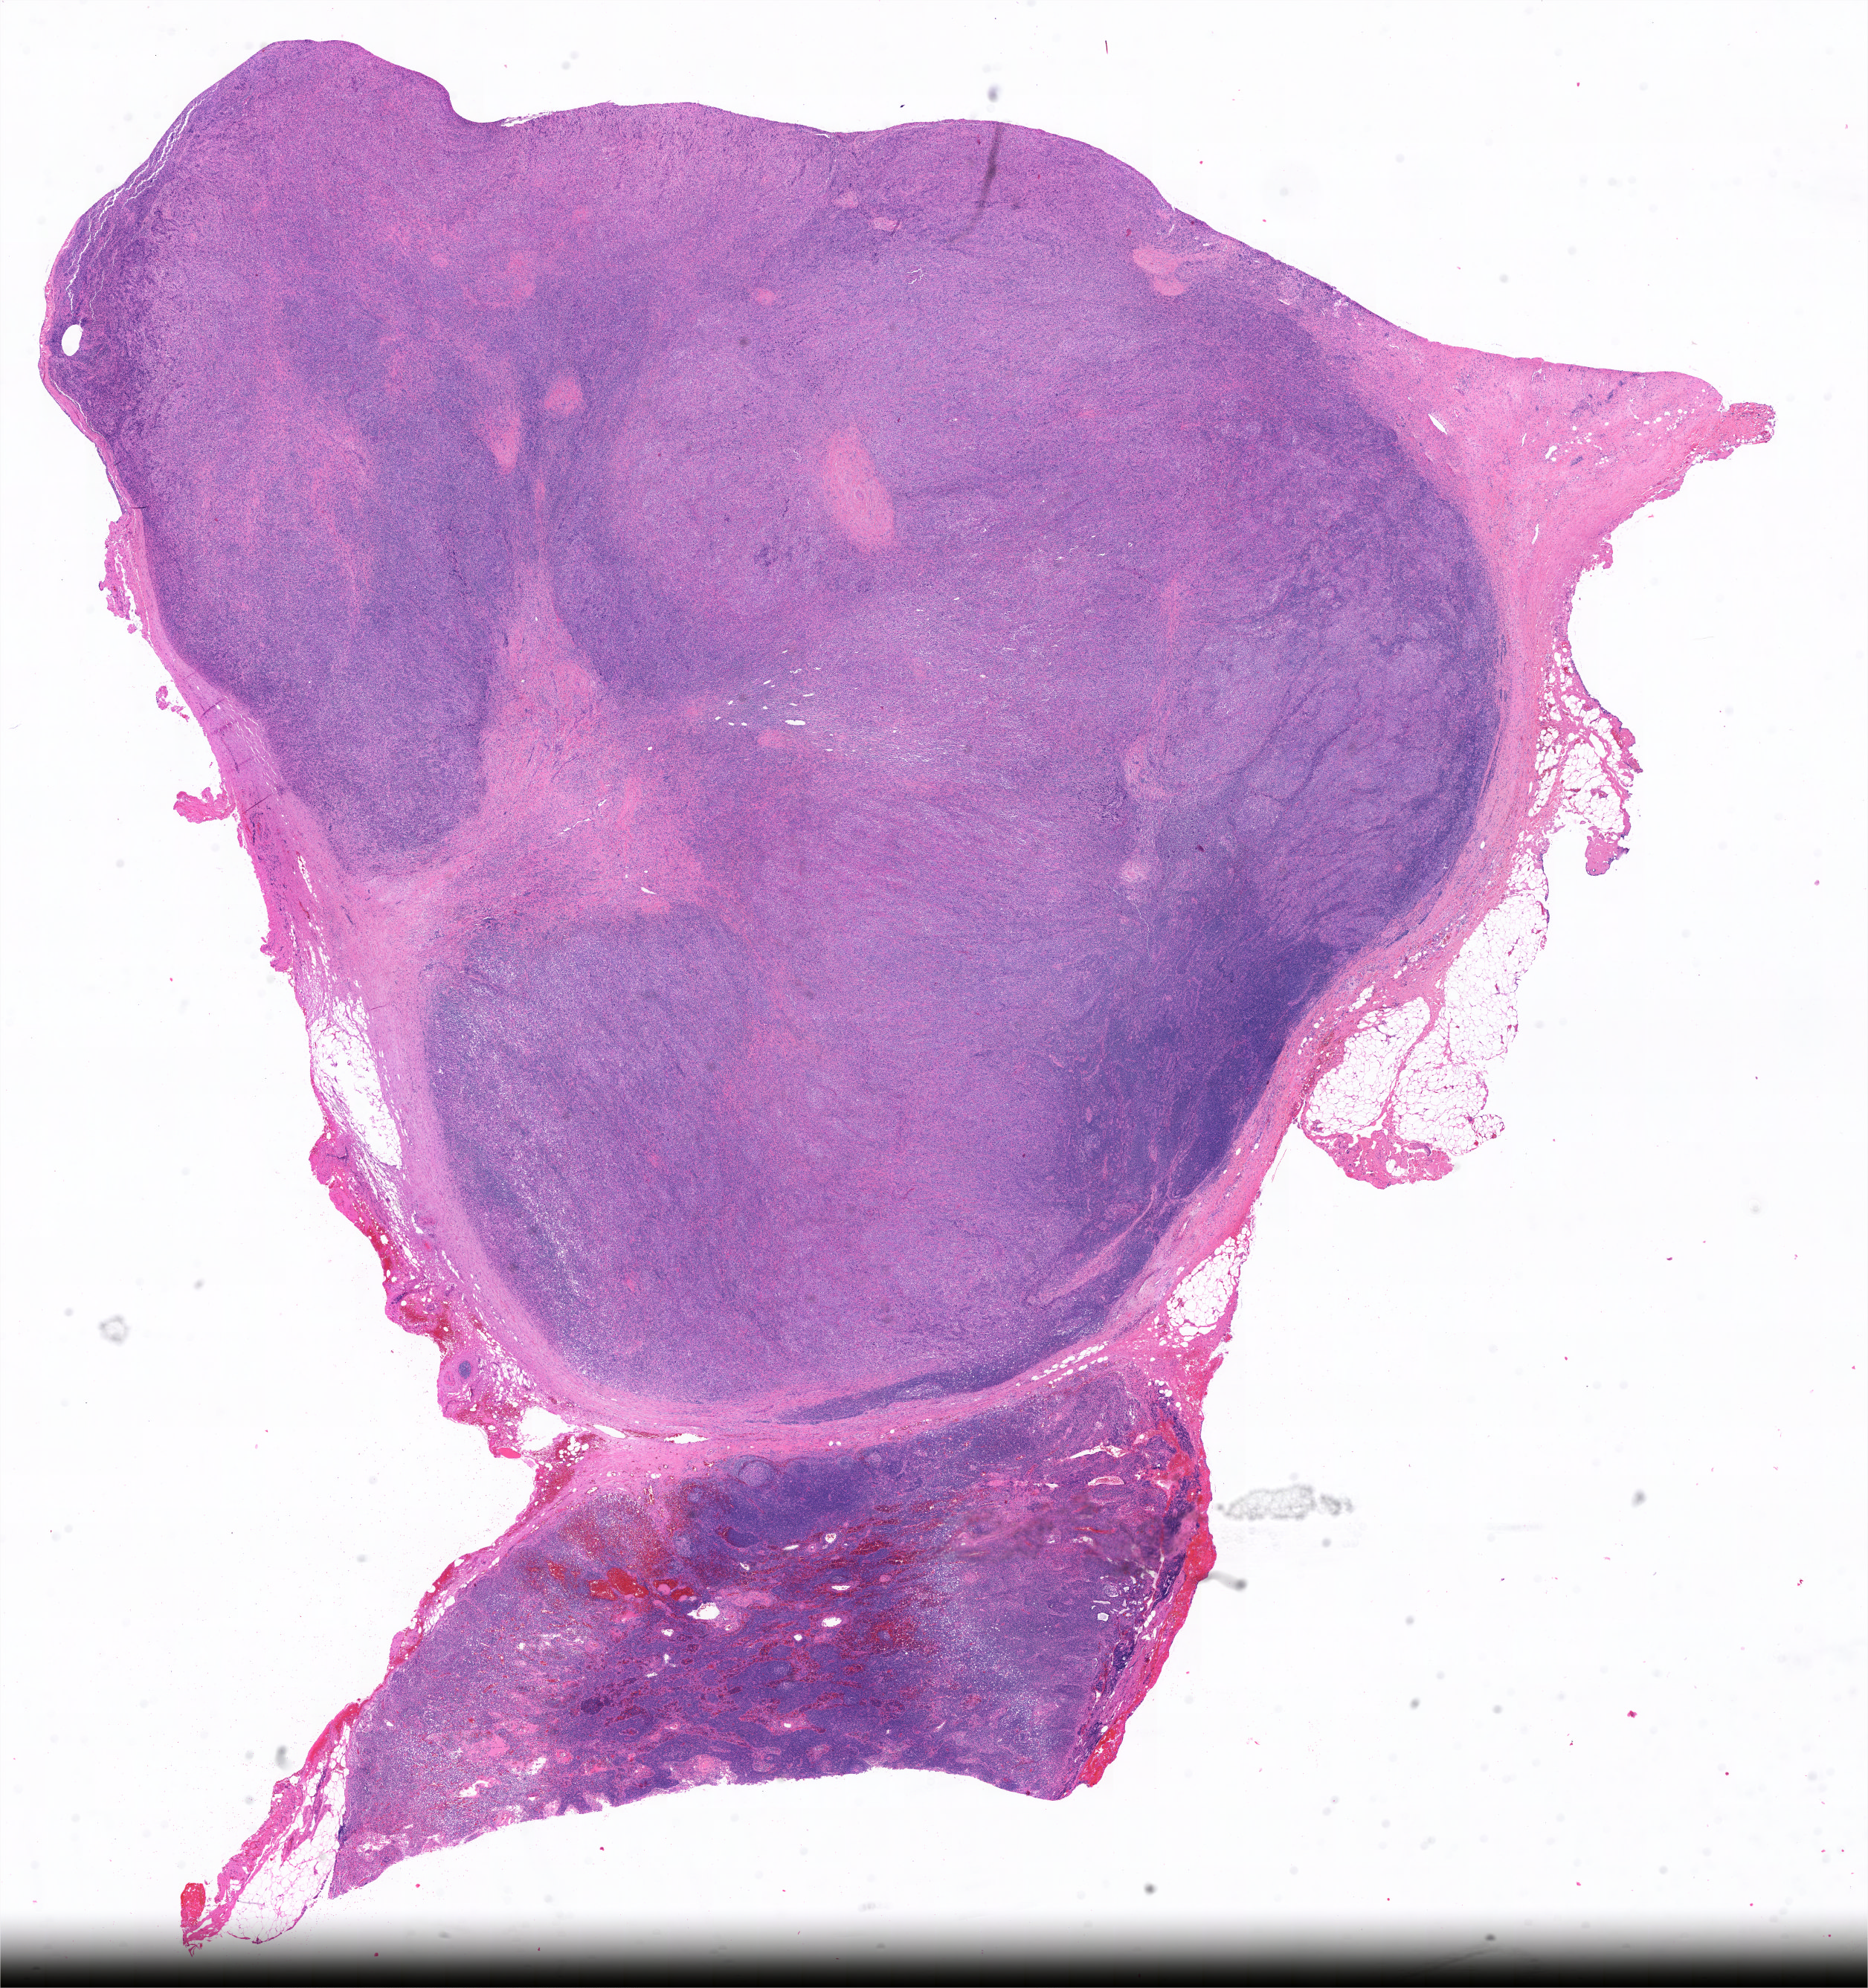
Digitized Hematoxylin and eosin (H&E) stained tissue section (whole slide) — low-resolution overview of the scanned area, about 18.7 x 19.9 mm; formalin-fixed paraffin-embedded (FFPE) diagnostic section; primary tumour sample from the lymphoid tissue. Female, age 46 years at initial diagnosis.
Histologic diagnosis: Diffuse large B-cell lymphoma, NOS (lymph nodes of head, face and neck).